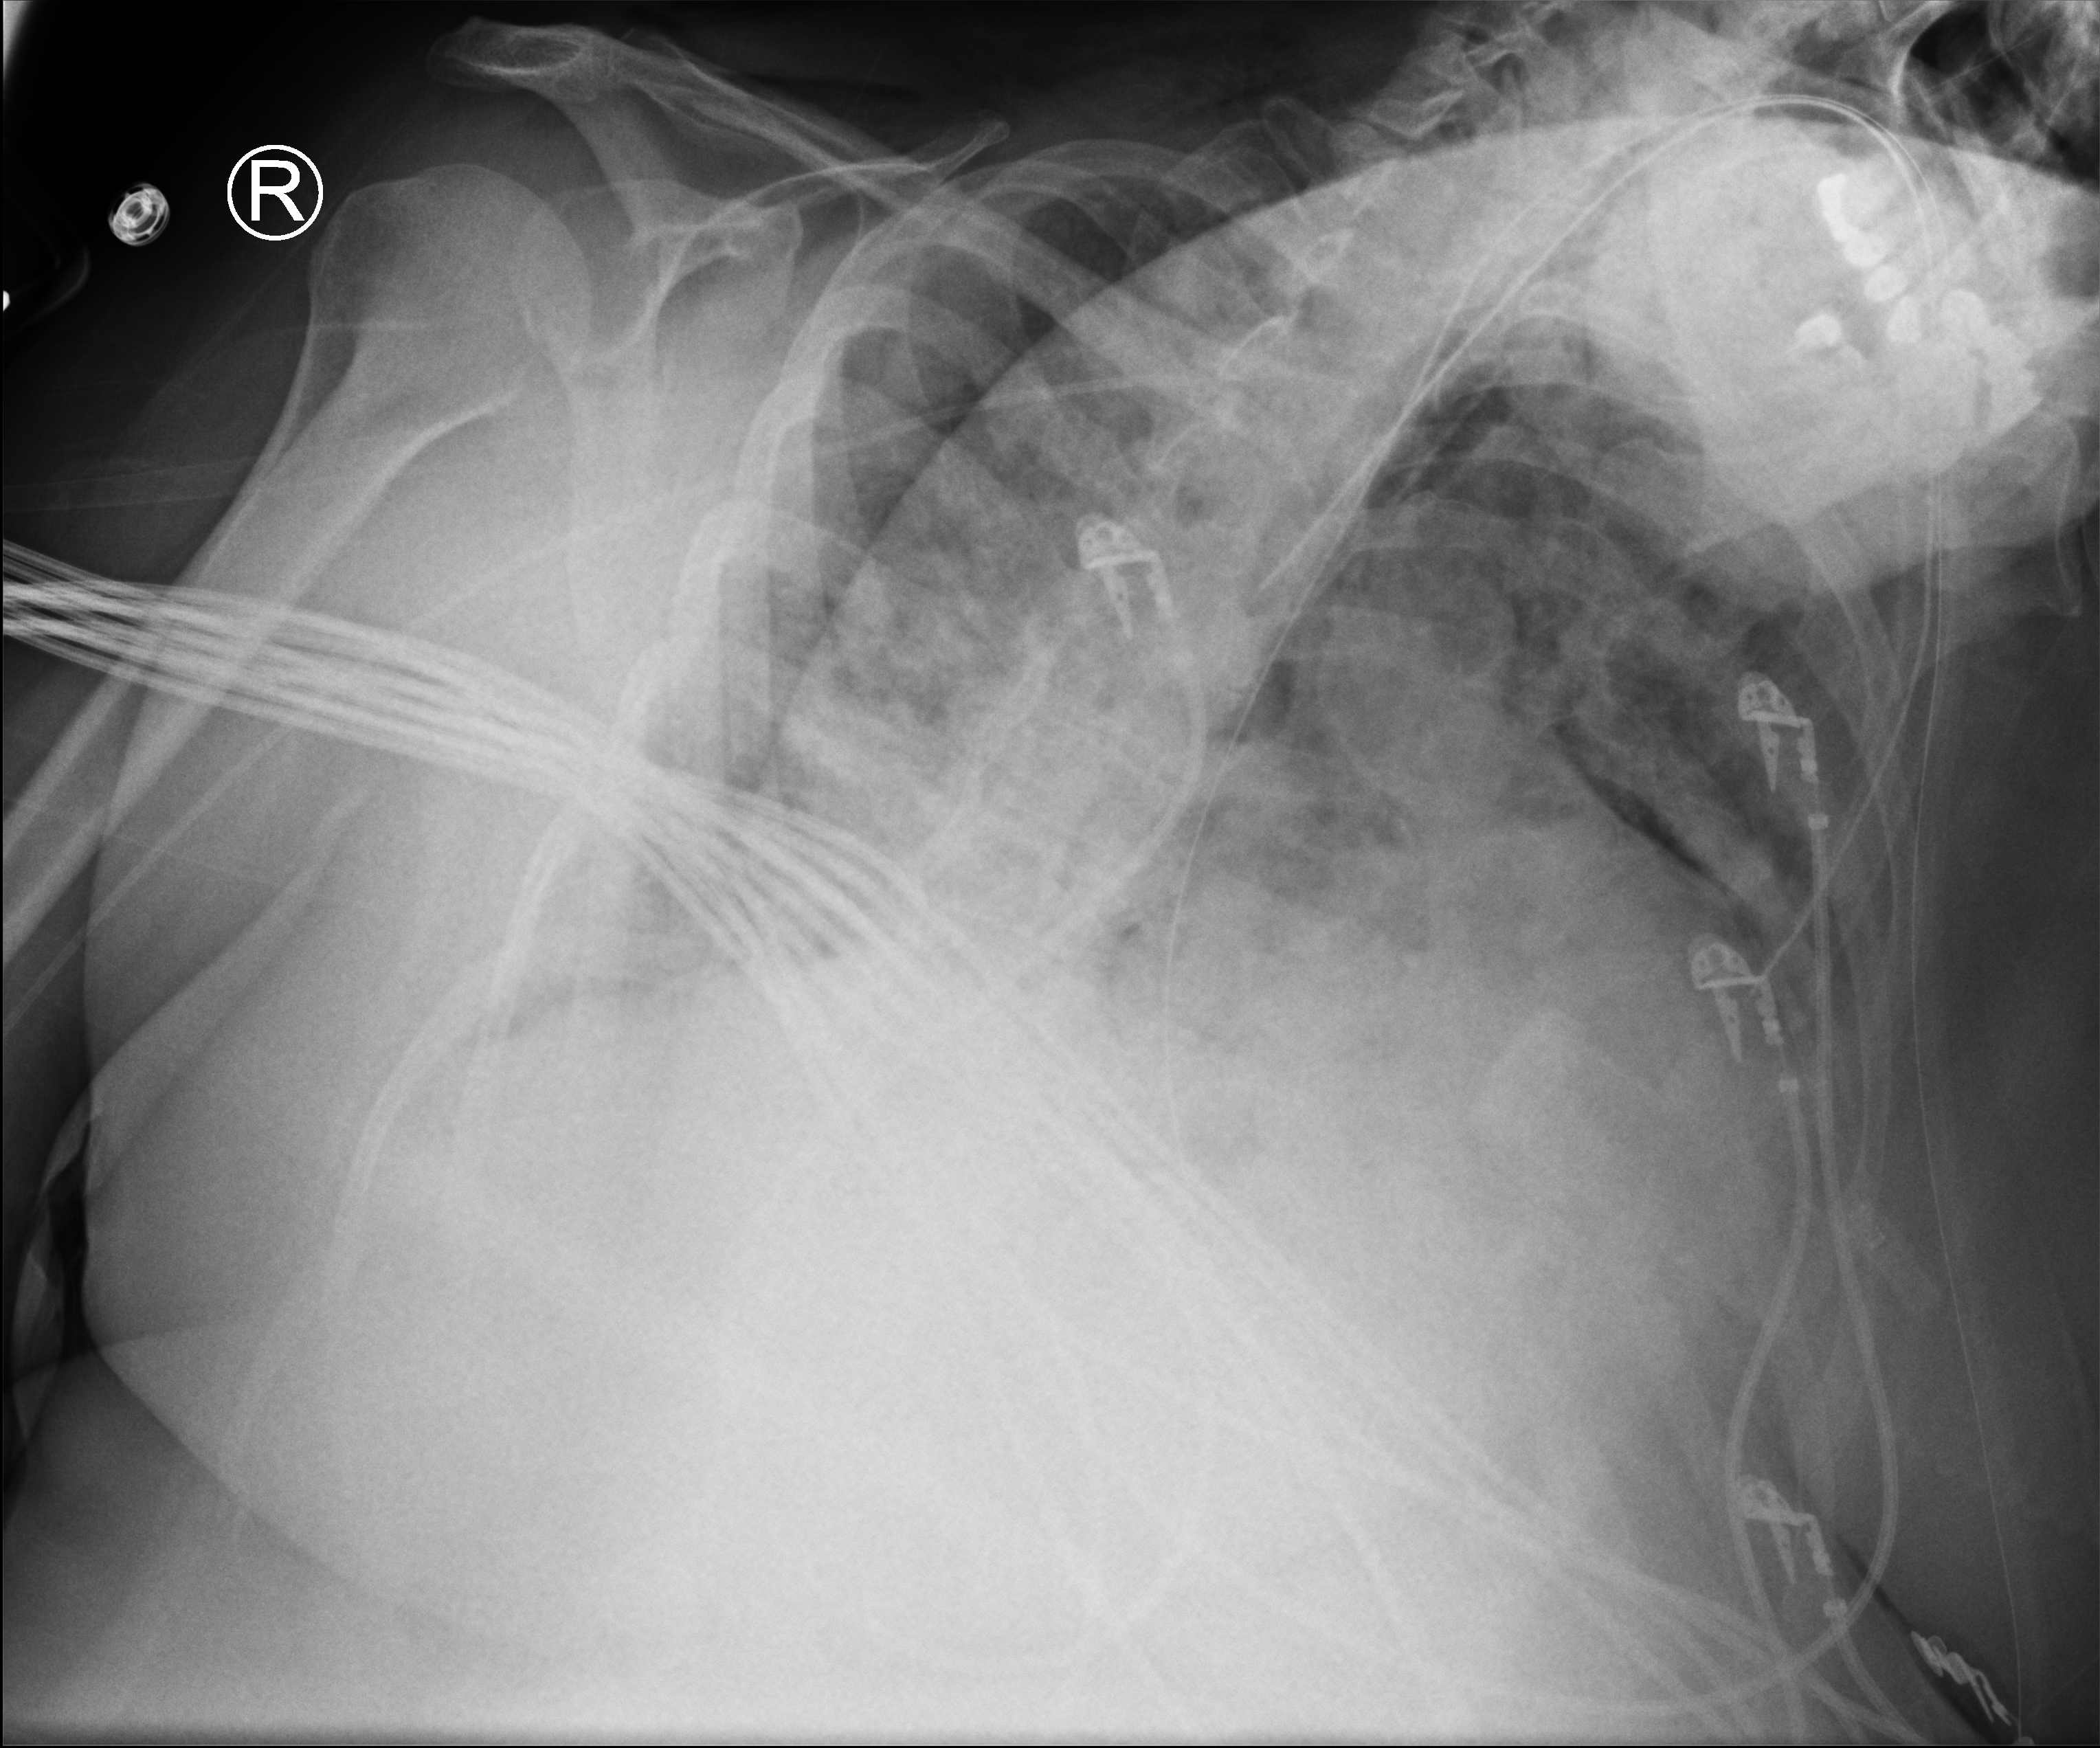
Chest X-ray (portable); anteroposterior (AP) projection. Patient hospitalised with COVID-19; female, aged 60–74 years.
Admission-level facts for this patient (not findings on this image; timing relative to this image not recorded): admitted to intensive care during this hospital stay: yes; chronic kidney disease (admission record): no; mechanically ventilated during this hospital stay: yes.